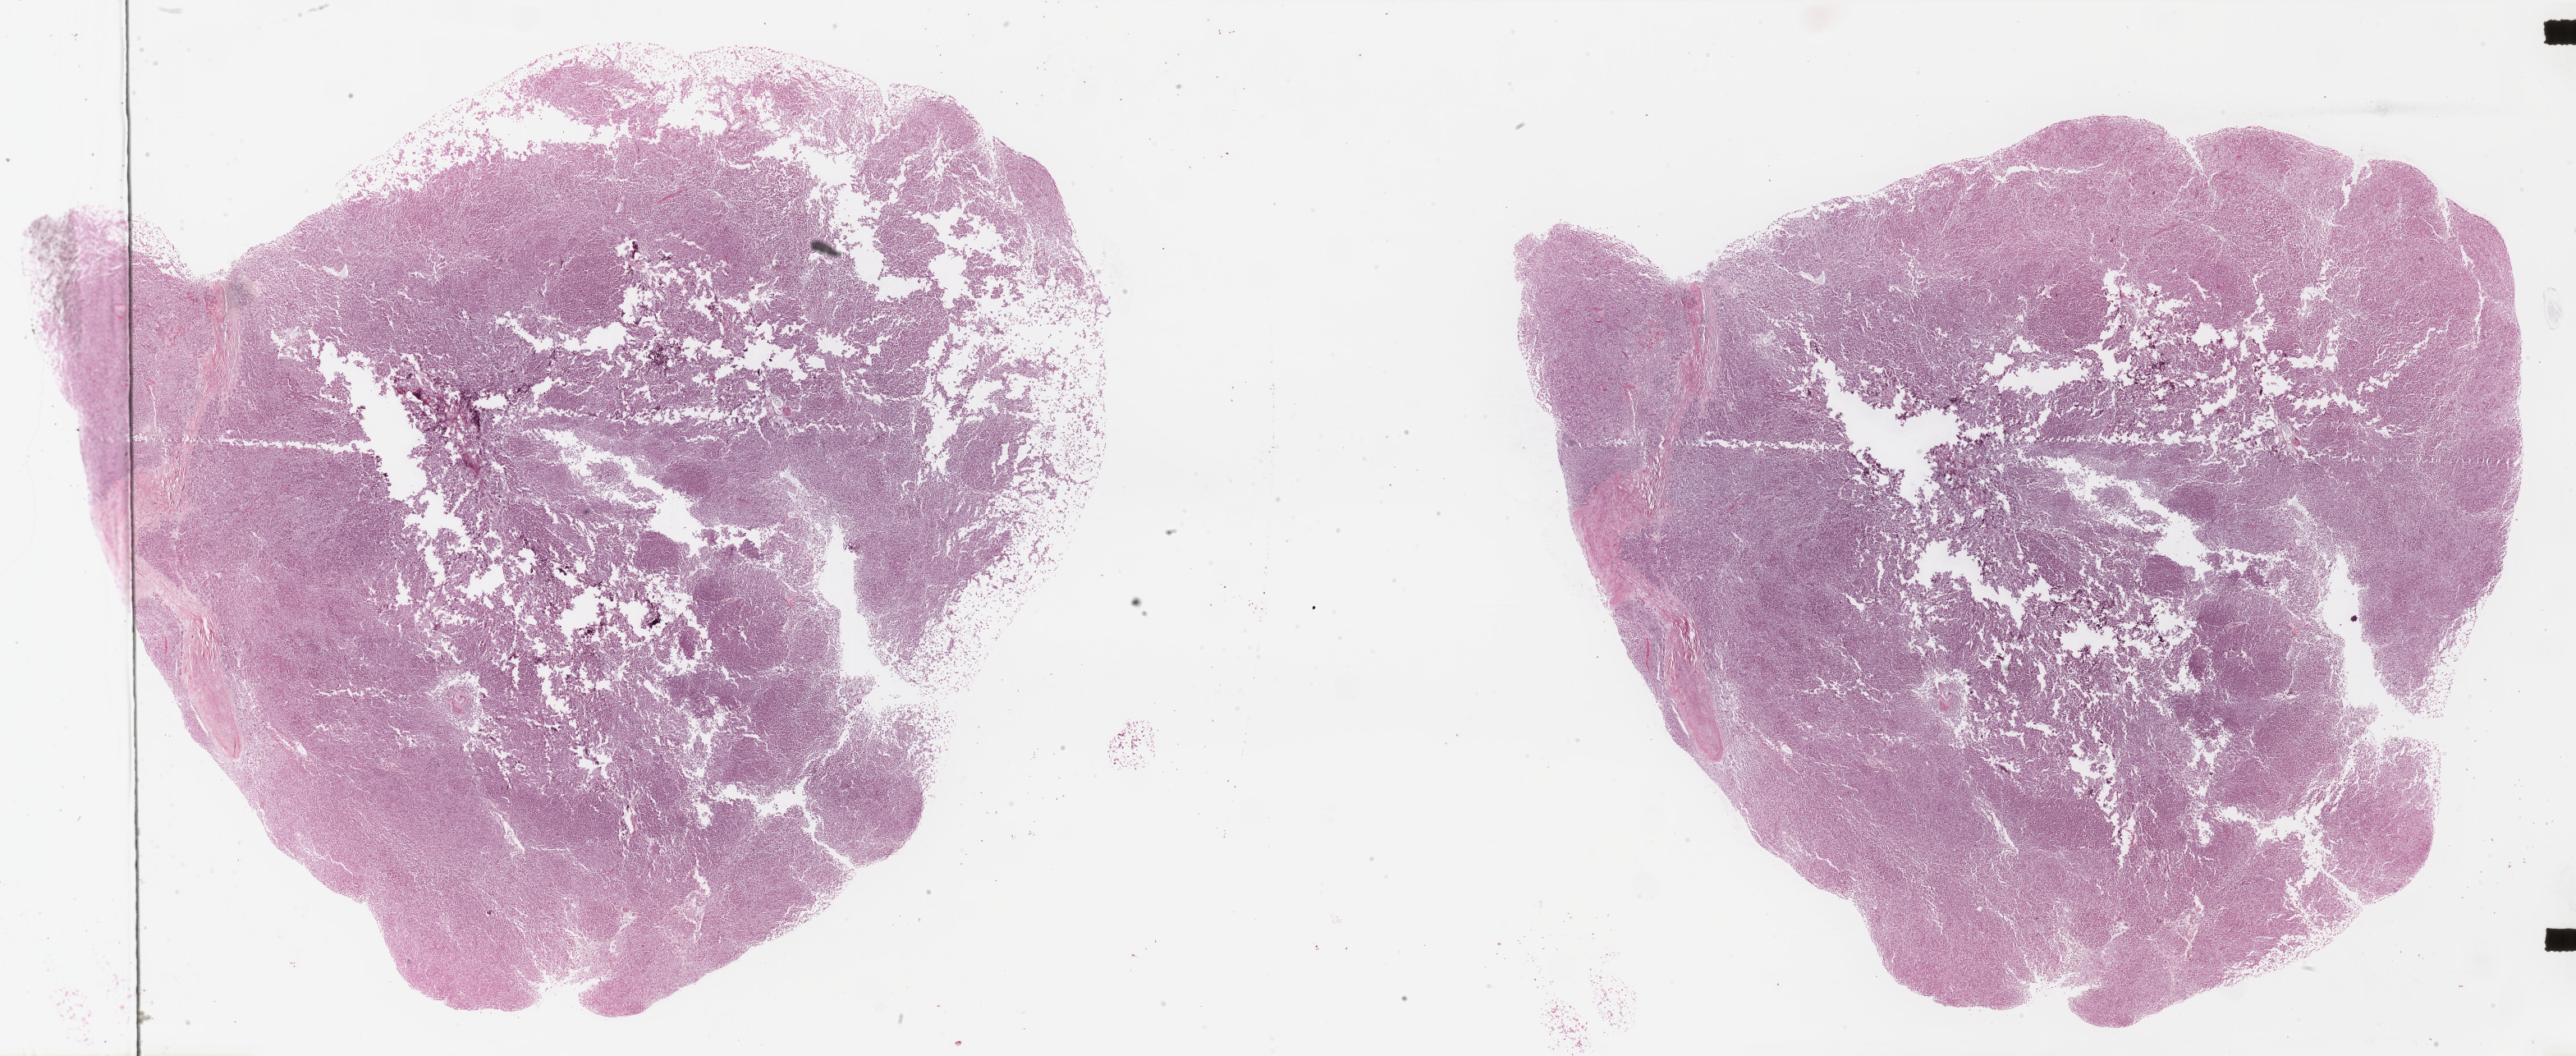
Whole-slide histology image, H&E-stained — low-resolution overview of the scanned area, about 49.7 x 20.3 mm; formalin-fixed paraffin-embedded (FFPE) diagnostic section; sample: primary tumour, kidney. Female, age 29 years at initial diagnosis.
Laterality: left. AJCC pathologic stage: I (7th edition). Lymph nodes positive (case pathology): 0 of 7 examined. Histologic diagnosis: Renal cell carcinoma, chromophobe type.